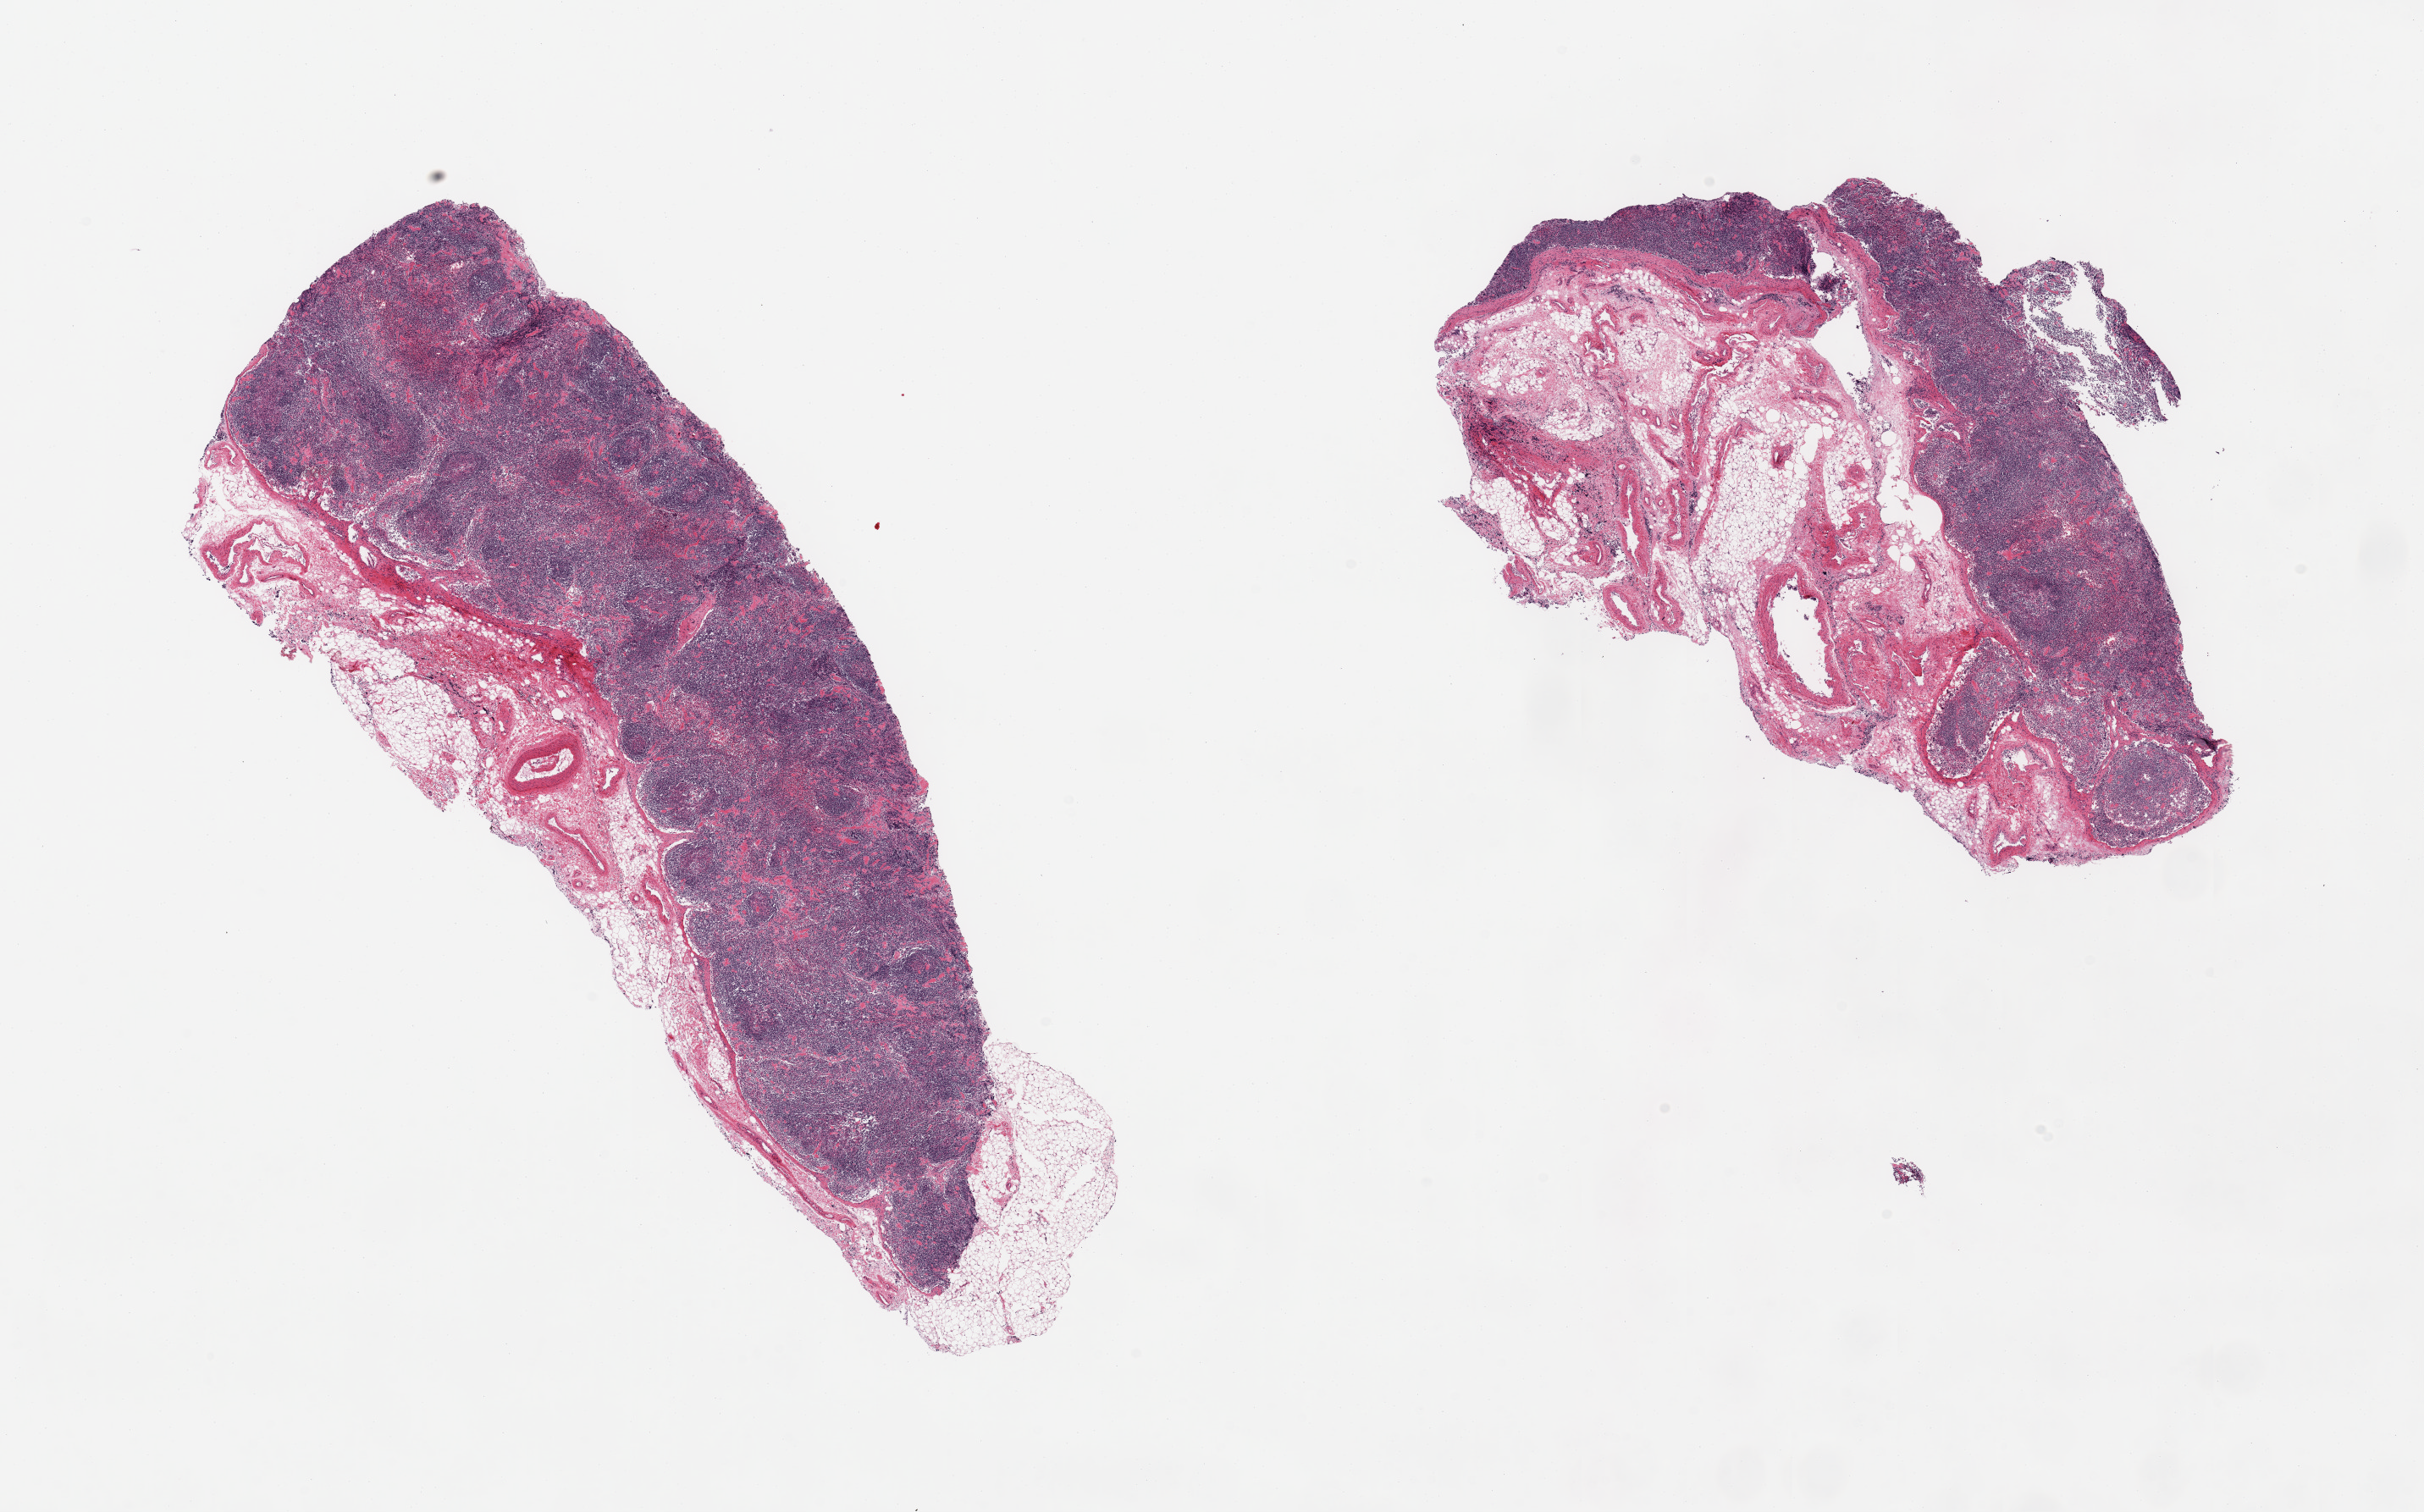
Whole-slide image, H&E stain — a low-resolution overview of the entire scanned area, about 22.6 x 14.1 mm; PAXgene-fixed paraffin-embedded (PFPE) section; section of ovary (target tissue); tissue donor sample. Female donor.
Reviewer comment on this tissue sample: 2 pieces; lymph node sampled not ovary.